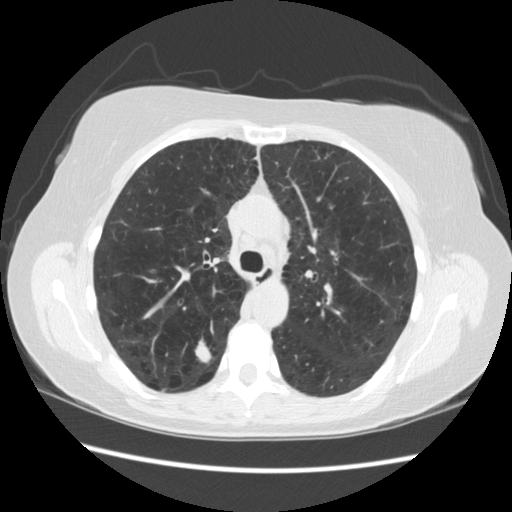
Low-dose screening chest CT, one axial slice; position 159 of 235 along the scan axis; reconstruction kernel STANDARD; 120 kVp; lung window (W 1500 / L -600 HU); 2.5 mm slice thickness; 512 × 512 image matrix.
Annotated regions visible in this slice (expert manual segmentation):
- lesion 1 (tumor, upper lobe of right lung): bounding box <195,337,211,361> (left, top, right, bottom; pixels)